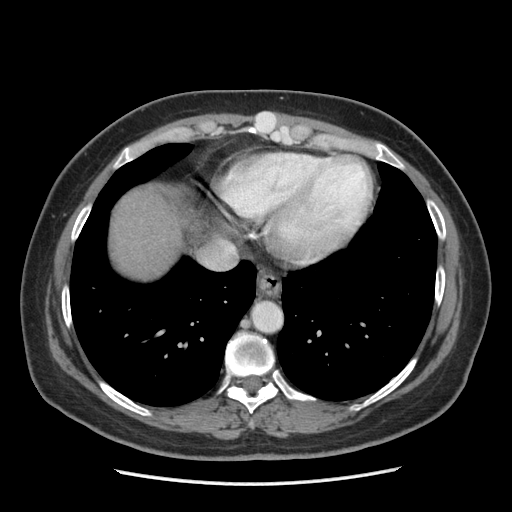
Contrast-enhanced abdominal CT (liver protocol), one axial slice. Slice 174 of 185 in the series (ordered by position). Soft-tissue window (W 400 / L 40 HU). 2.5 mm slice thickness. 512 × 512 image matrix. Case-level facts recorded for this patient, not image findings: diagnosis: hepatocellular carcinoma (patient treated with transarterial chemoembolisation; whether this scan precedes or follows treatment is not stated here); TNM stage (as recorded): Stage-I; Child-Pugh class: A.
Structures marked on this image (semi-automatic segmentation, software-assisted and operator-edited):
- liver parenchyma outside the tumour (the mass and vessels are separate outlines, so this box may not span the whole liver): box from (x=112, y=188) to (x=198, y=278) px